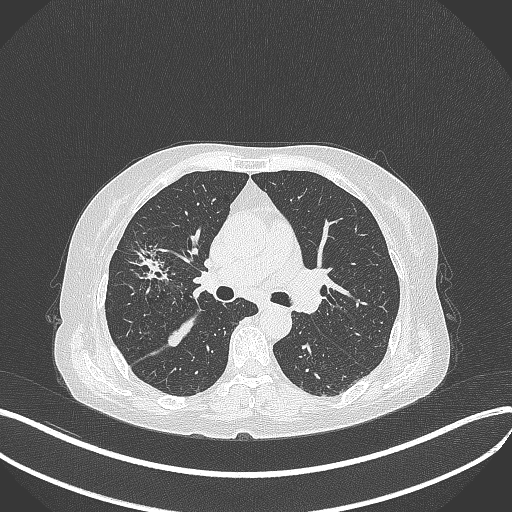
Chest CT, one axial slice; slice 238 of 429 in the series (ordered by position); 120 kVp; lung window (W 1500 / L -600 HU); 512 × 512 image matrix, field of view 400 × 400 mm. Patient: female, 69 years. From the clinical record (not read from this slice): clinical TNM (as recorded): T1b N3 M0.
Annotated regions visible in this slice (rectangle marked by the reading radiologist):
- lung tumour (recorded histology: small cell carcinoma): bounding box <125,243,178,290> (left, top, right, bottom; pixels)